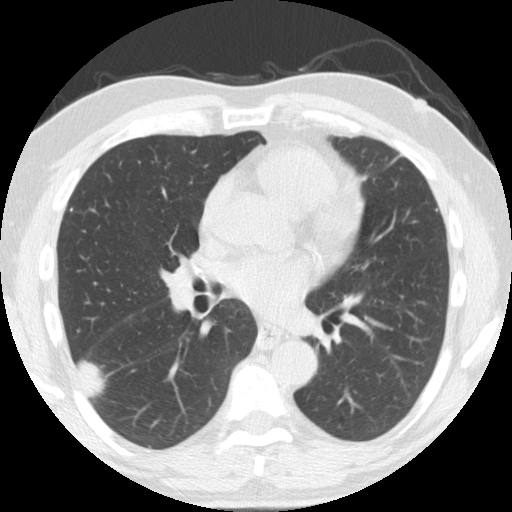
Chest CT (low-dose screening protocol), one axial image. Second screening round (one year after baseline). Lung window (W 1500 / L -600 HU). 2.5 mm slice thickness. 120 kVp. 512 × 512 image matrix, field of view 341 × 341 mm. Male participant, aged 61 years at enrolment. Former smoker at enrolment.
• Lesion marked by an expert reader, bounding box (x1, y1, x2, y2) in pixels: (54, 329, 121, 403).
• The exam's reader record, not a measurement of the box and not confirmed to be the same lesion: non-calcified nodule or mass ≥4 mm, right lower lobe, 33 × 19 mm, smooth margins, soft tissue attenuation, pre-existing on the prior screen: yes; interval growth: yes.